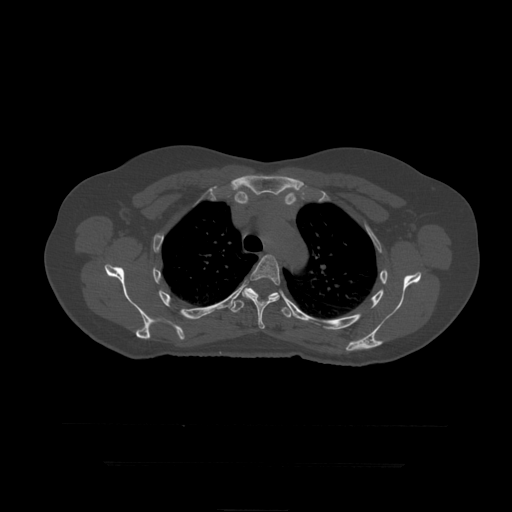
CT including the spine, one axial slice; slice 331 of 399 in the series (ordered by position); reconstruction kernel STANDARD; bone window (W 1800 / L 400 HU); 1.25 mm slice thickness; 512 × 512 image matrix, field of view 450 × 450 mm. Patient age 41 years. From the clinical record (not read from this slice): primary cancer: breast.
Structures marked on this image (semi-automatically segmented with operator editing):
- T5 vertebra: bounding box [x1, y1, x2, y2] px = [242, 255, 280, 329]
- T6 vertebra: [231, 288, 291, 318]